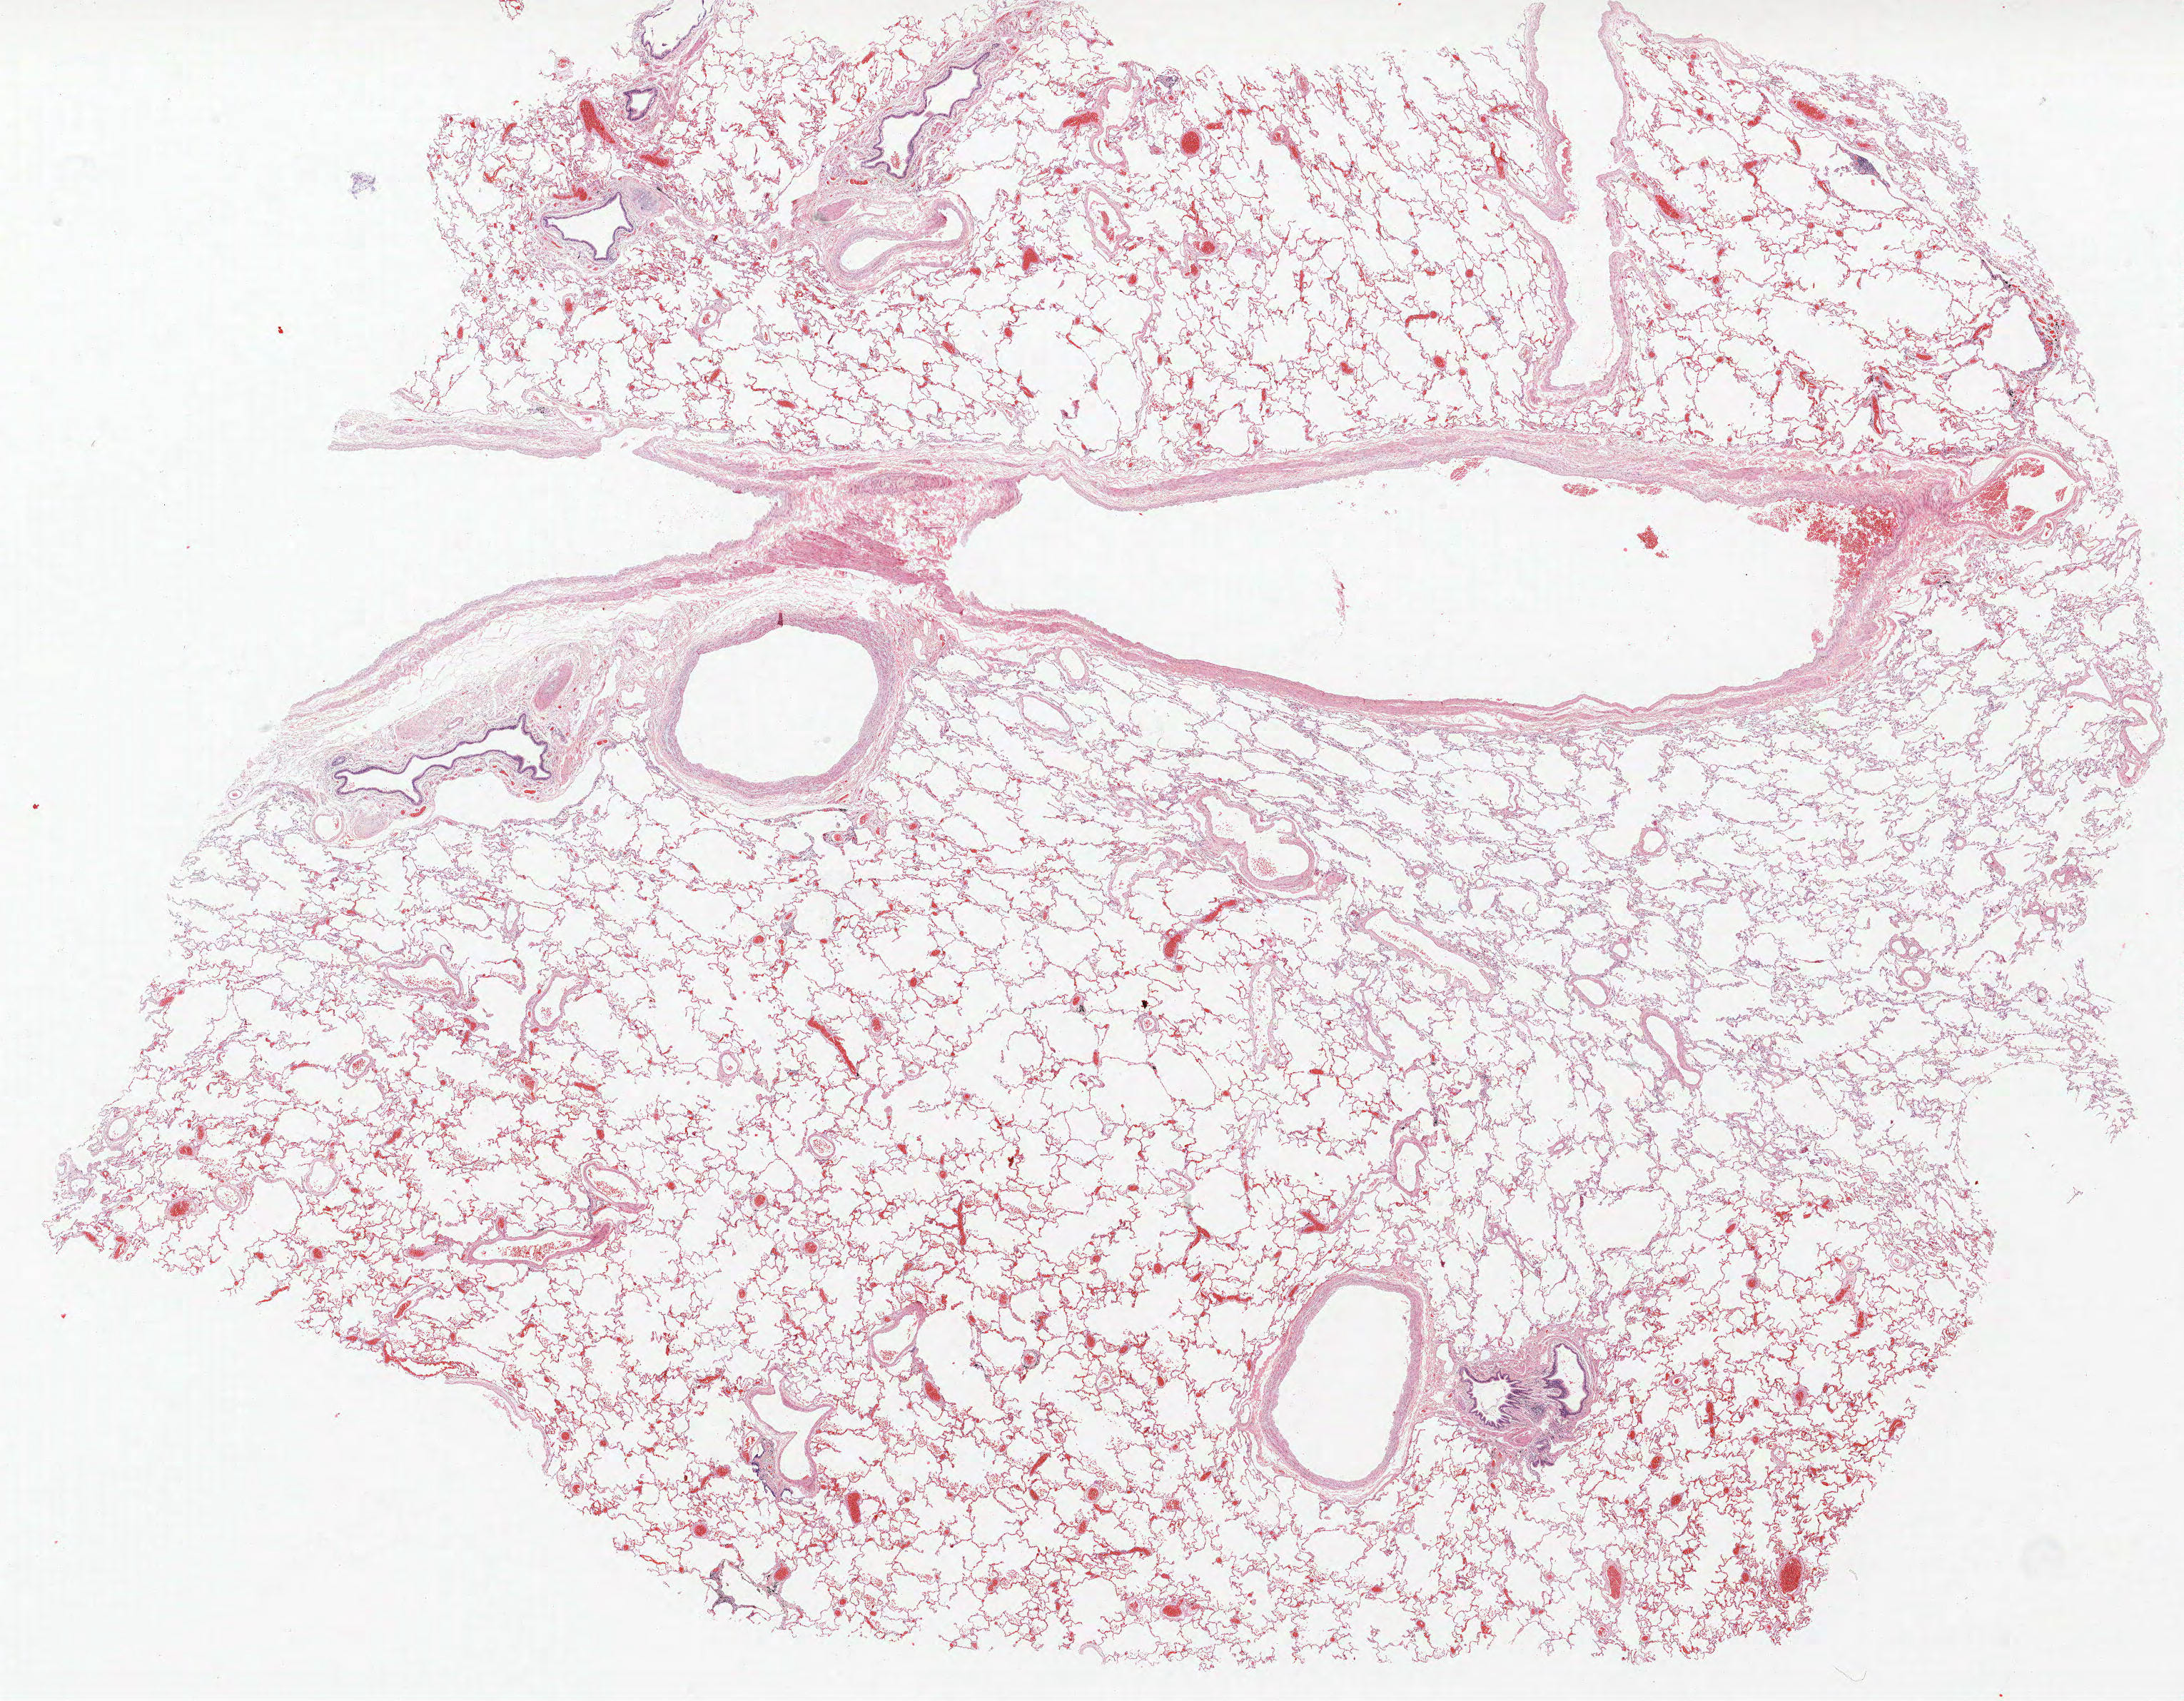
Hematoxylin and eosin (H&E) stained whole-slide image — low-resolution overview of the scanned area, about 24.5 x 19.1 mm. Formalin-fixed paraffin-embedded (FFPE) section. Lung. Male patient, aged 60 at enrolment. Former smoker at enrolment. Grade: poorly differentiated (G3).
* tumour size (pathology): 35 mm
* participant's lung-cancer diagnosis: Adenocarcinoma, NOS
* primary tumour location (clinical record): right lower lobe
* stage (AJCC 6th edition): IIB